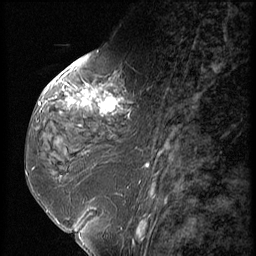
Breast MRI (dynamic contrast-enhanced), one sagittal slice; position 26 of 56 along the scan axis; dynamic contrast-enhanced series, image 2 of 3 at this slice position (ordered by acquisition); 1.5 T; TE 4.2 ms, TR 9 ms; 2.5 mm slice thickness; 256 × 256 image matrix. Patient: female, 59 years. From the clinical record (not read from this slice): setting: breast cancer imaged before/during neoadjuvant chemotherapy; receptor status: HER2-positive.
Structures marked on this image (semi-automatic segmentation, software-assisted and operator-edited):
- analysis volume of interest (the breast-tissue region the enhancement analysis was run in; not a lesion): bounding box (x1, y1, x2, y2) in pixels: (44, 66, 151, 135)
- tumour enhancement mask (voxels above the 140 % enhancement threshold inside the analysis volume of interest): (56, 77, 120, 113)